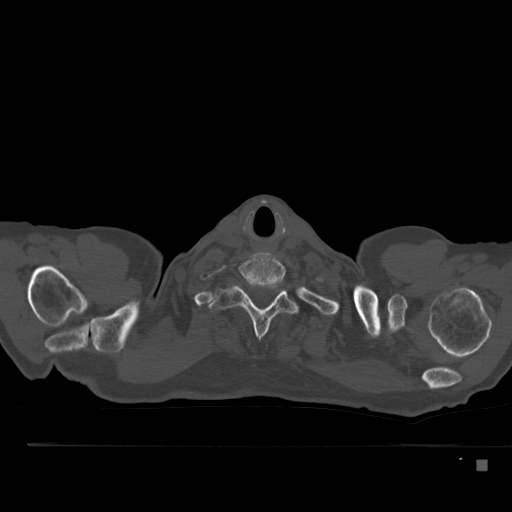
CT including the spine, one axial slice. Slice 429 of 517 in the series (ordered by position). 120 kVp. Bone window (W 1800 / L 400 HU). 1.5 mm slice thickness. 512 × 512 image matrix, field of view 408 × 408 mm. Male patient, age 70 years. From the clinical record (not read from this slice): primary cancer: renal.
Outlined on this slice (semi-automatic segmentation, software-assisted and operator-edited):
- T1 vertebra: bounding box [x1, y1, x2, y2] px = [209, 284, 297, 338]